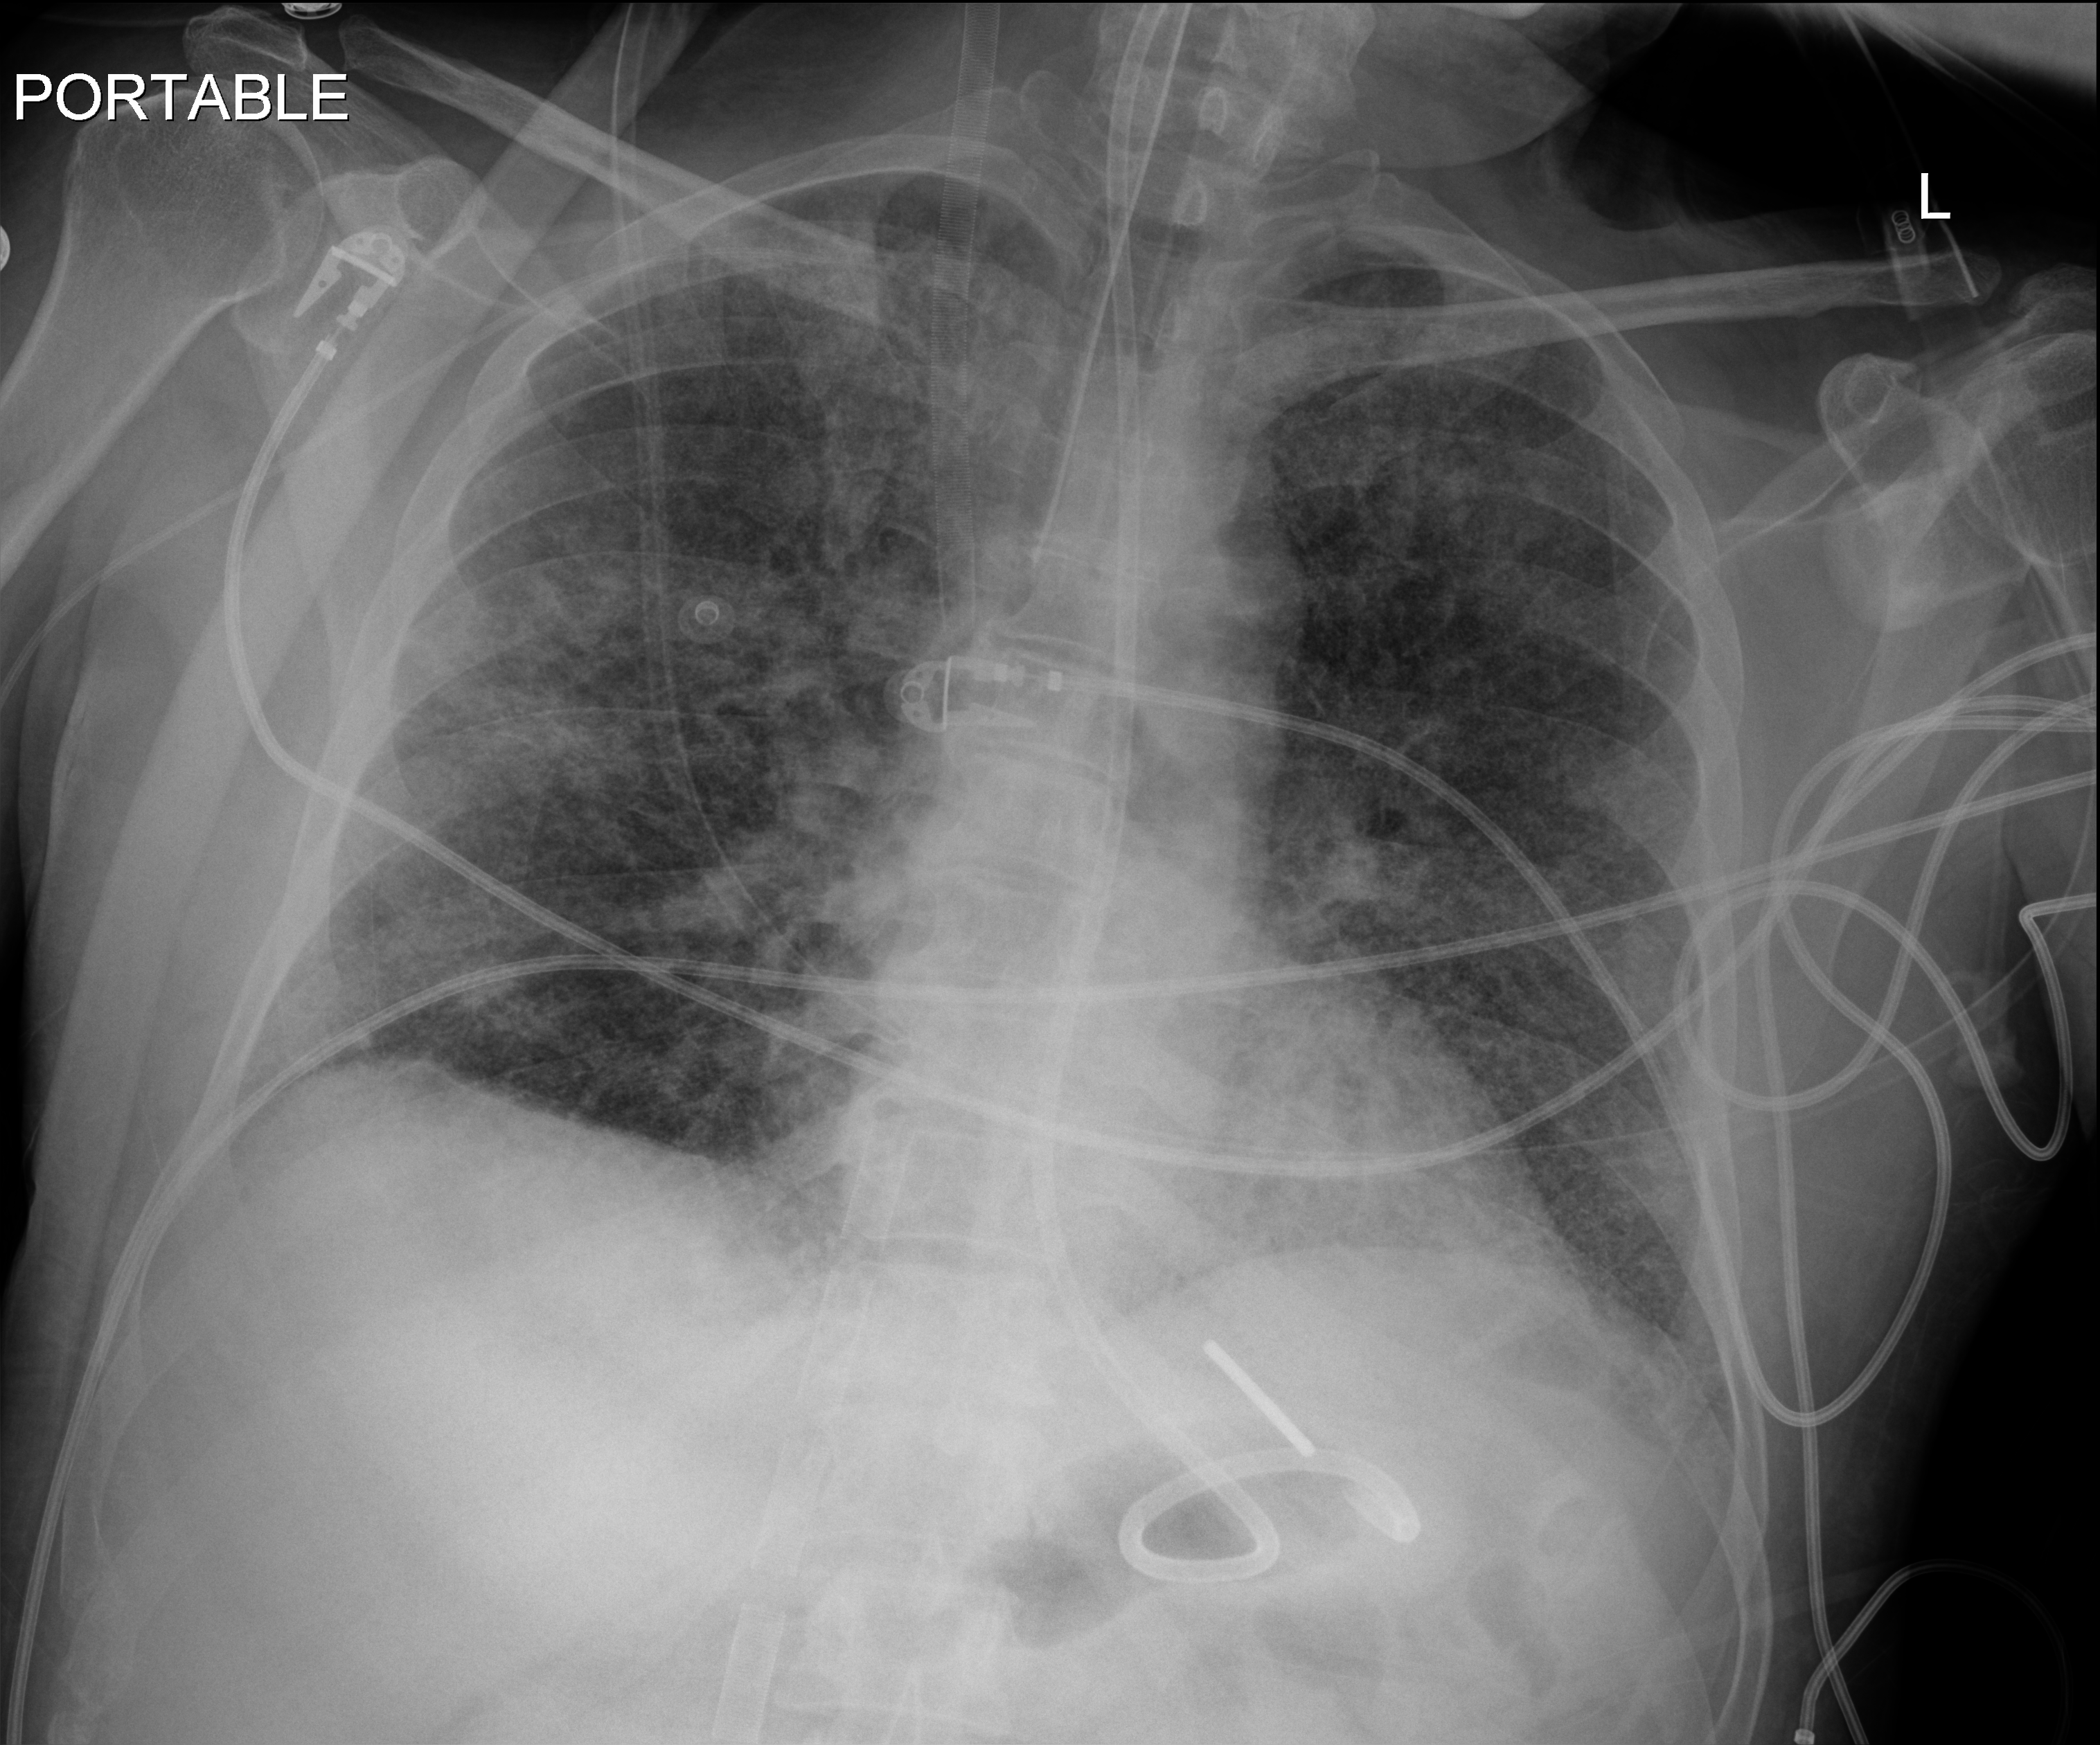
Chest X-ray (portable). Male patient hospitalised with COVID-19, age 18–59 years.
Hospital-stay facts (about this admission, not read from this image; timing relative to this image not recorded):
- length of hospital stay: 42 days
- admitted to intensive care during this hospital stay: yes
- mechanically ventilated during this hospital stay: yes